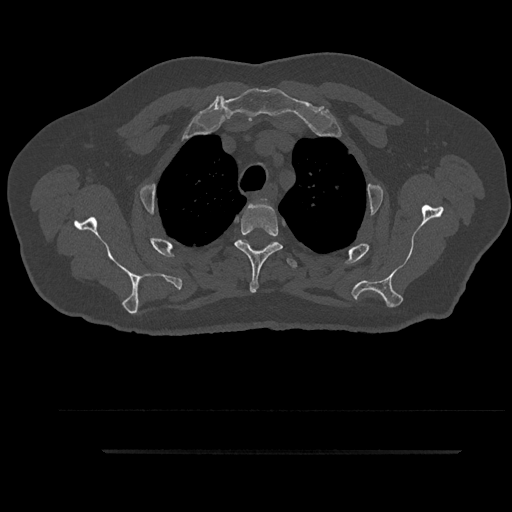
CT including the spine, one axial slice; slice 712 of 797 in the series (ordered by position); reconstruction kernel Br40s/3; bone window (W 1800 / L 400 HU); 0.5 mm slice thickness; 512 × 512 image matrix. Male patient, age 63 years. Case-level facts recorded for this patient, not image findings: primary cancer: renal; vertebrae with lytic lesions (as recorded): T8.
Annotated regions visible in this slice (semi-automatically segmented with operator editing):
- T2 vertebra: box from (x=268, y=201) to (x=271, y=205) px
- T3 vertebra: (x=234, y=202)–(x=283, y=293)
- T4 vertebra: (x=244, y=240)–(x=298, y=269)